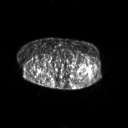
FDG PET of an extremity soft-tissue mass (from a PET/CT study), one axial slice. 3.27 mm slice thickness. 128 × 128 image matrix, field of view 700 × 700 mm. Patient: female, 62 years. Case-level facts recorded for this patient, not image findings: histological type: undifferentiated – high grade; grade: high; site of the primary tumour: left thigh.
Annotated regions visible in this slice (expert contour drawn on MRI and transferred to this co-registered scan by the dataset authors):
- gross tumour volume including surrounding oedema: bounding box <89,71,93,75> (left, top, right, bottom; pixels)